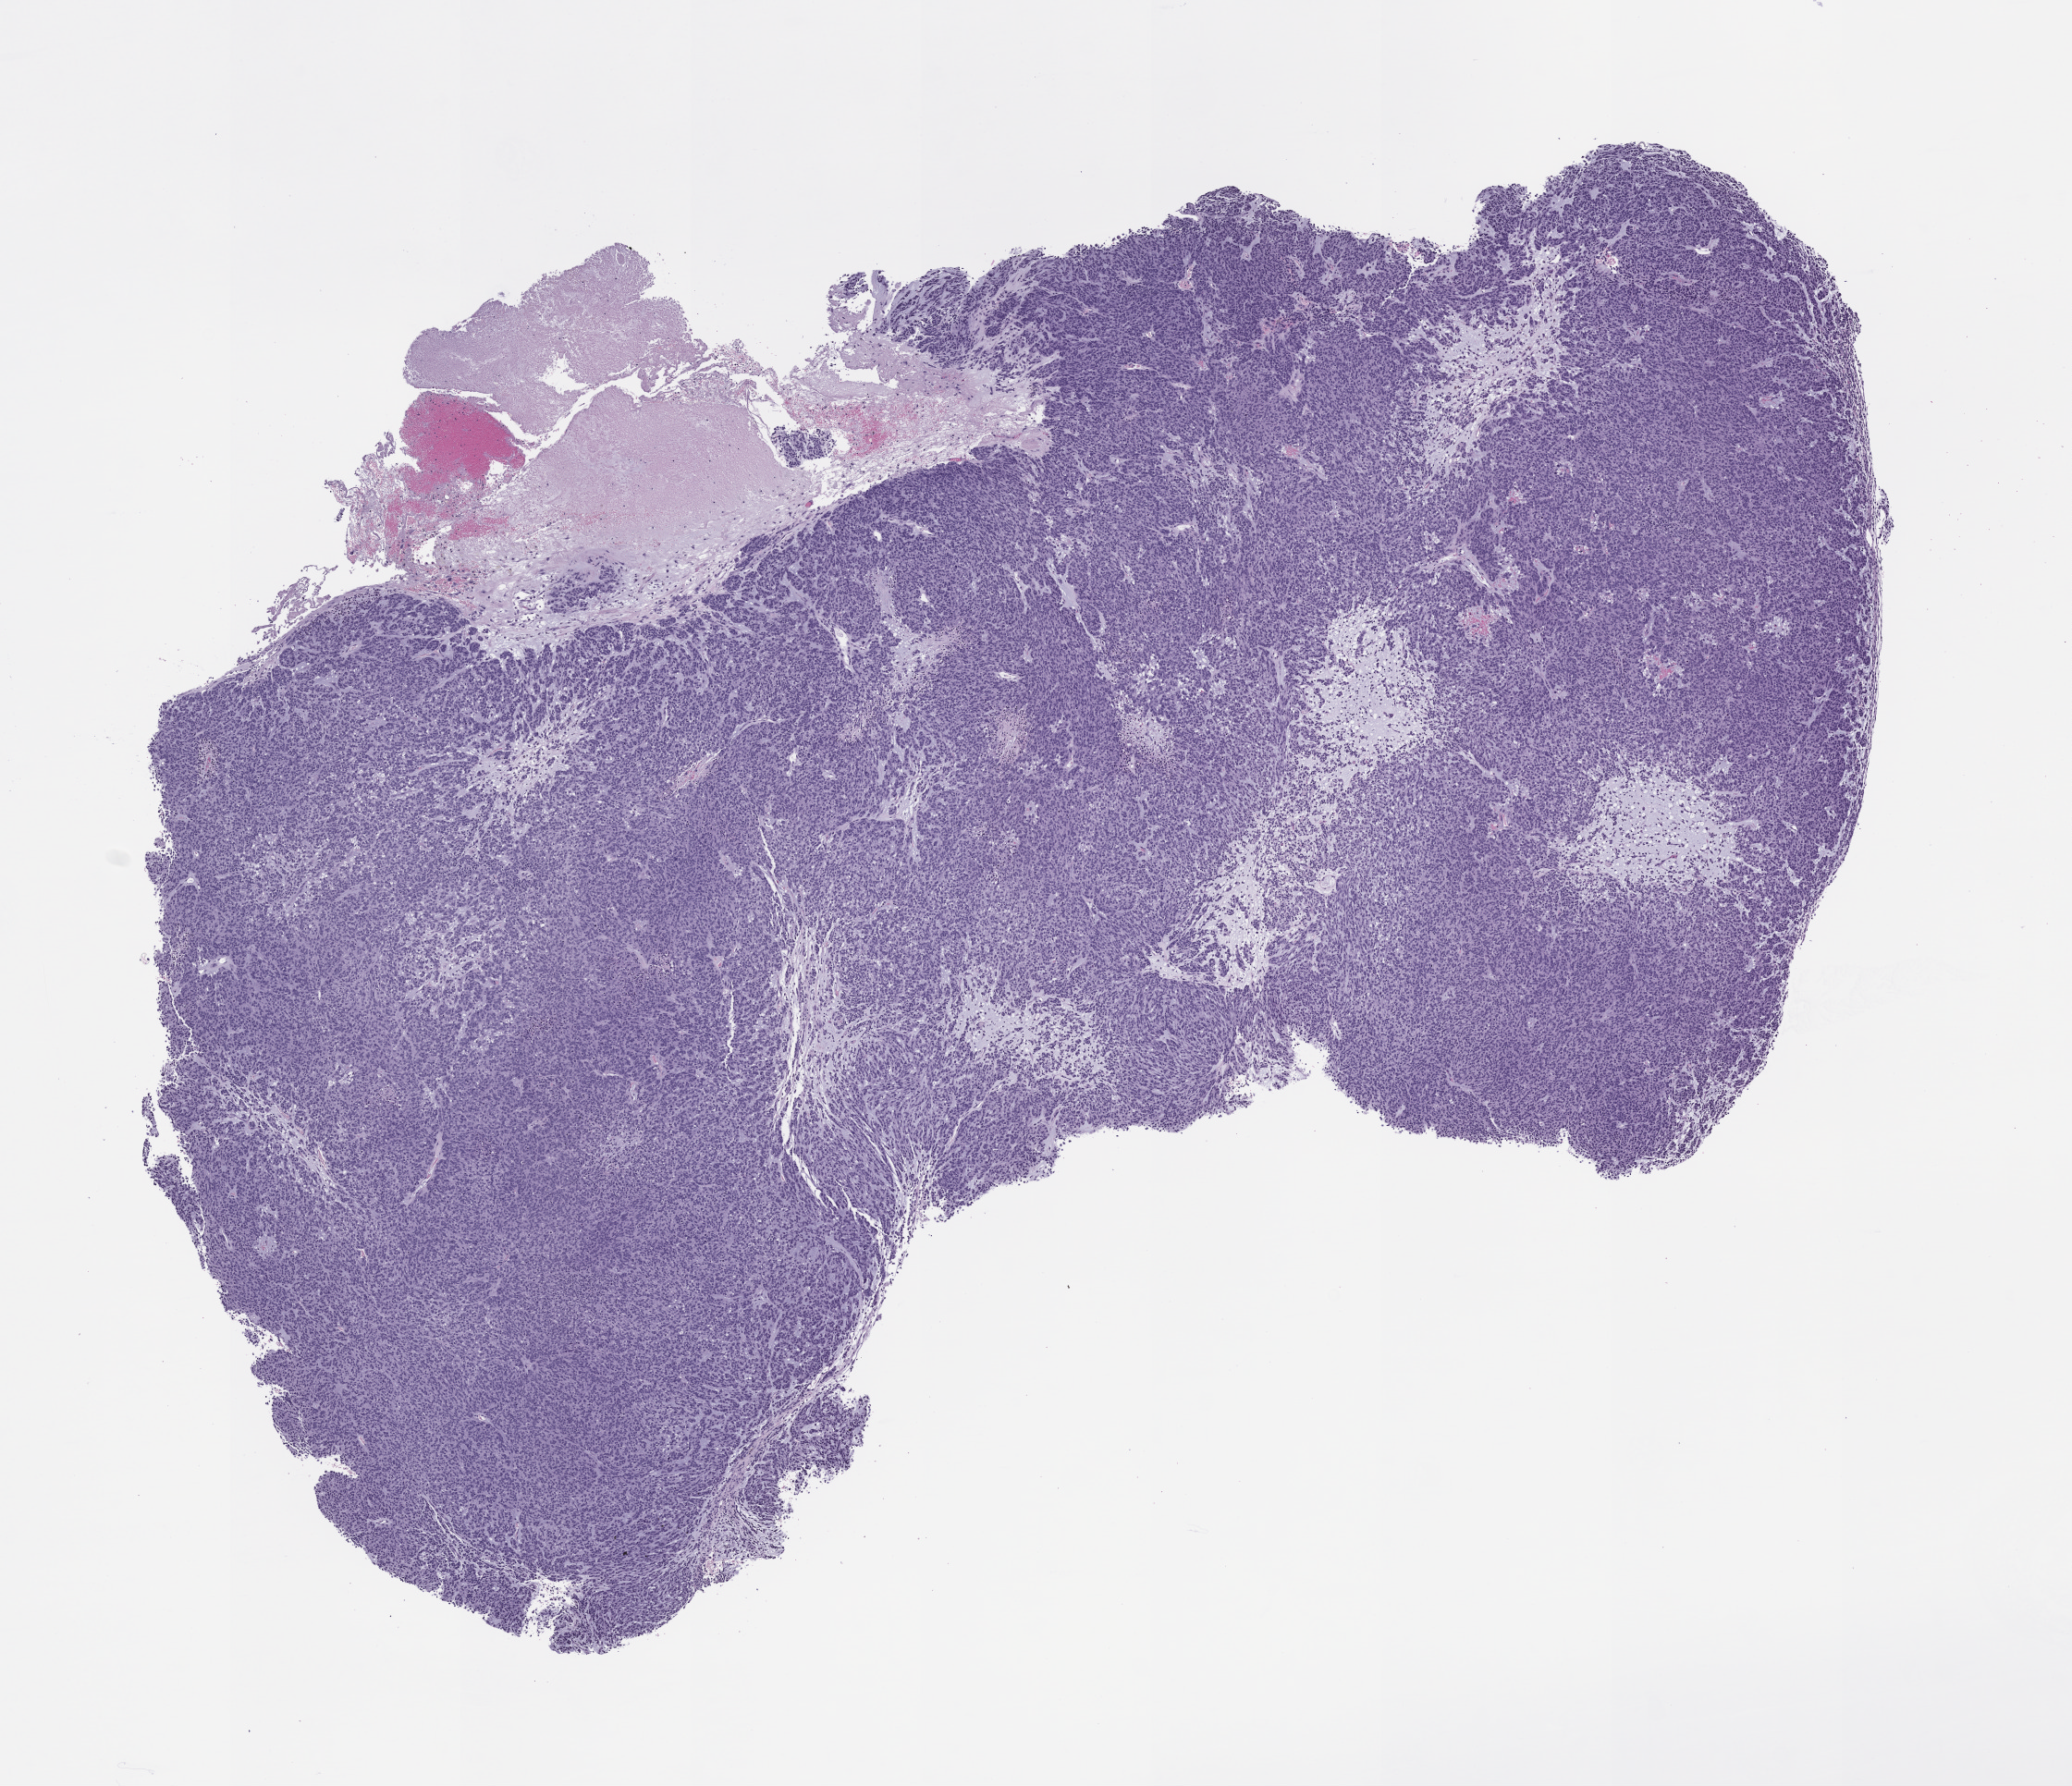
Hematoxylin and eosin (H&E) whole-slide image of a patient-derived xenograft (PDX) tumor grown in a mouse, passage 0 — low-resolution overview of the scanned area, about 9.0 x 7.8 mm, formalin-fixed, paraffin-embedded (FFPE) tissue, originating tumor site category: gastrointestinal tract.
Originating patient diagnosis: Gastrointestinal Stromal Tumor.